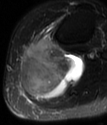
MRI of an extremity soft-tissue mass, one axial slice. Position 40 of 78 along the scan axis. T2-weighted fat-saturated. MR volume resampled by the dataset authors to the PET/CT grid (not the native acquisition matrix). 3.27 mm slice thickness. 107 × 125 image matrix. Female patient. Case-level facts recorded for this patient, not image findings: histological type: extraskeletal high grade osteogenic sarcoma; grade: high; site of the primary tumour: left calf.
Outlined on this slice (expert contour drawn on MRI and transferred to this co-registered scan by the dataset authors):
- gross tumour volume (mass): box from (x=19, y=36) to (x=84, y=99) px